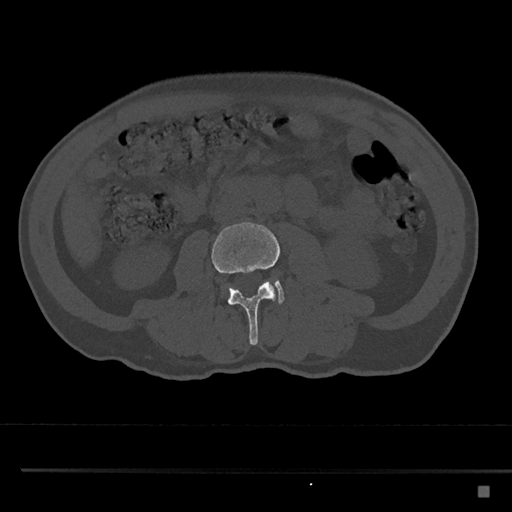
CT including the spine, one axial slice; position 685 of 797 along the scan axis; 120 kVp; bone window (W 1800 / L 400 HU); 0.5 mm slice thickness; 512 × 512 image matrix, field of view 391 × 391 mm. Male patient, age 59 years. Case-level facts recorded for this patient, not image findings: primary cancer: prostate.
Outlined on this slice (semi-automatically segmented with operator editing):
- L3 vertebra: box from (x=211, y=221) to (x=280, y=345) px
- L4 vertebra: (x=222, y=279)–(x=285, y=304)